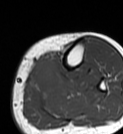
MRI of an extremity soft-tissue mass, one axial slice; slice 18 of 68 in the series (ordered by position); MR volume resampled by the dataset authors to the PET/CT grid (not the native acquisition matrix); 3.27 mm slice thickness; 123 × 134 image matrix, field of view 120 × 131 mm. Female patient. From the clinical record (not read from this slice): histological type: extraskeletal high grade osteogenic sarcoma; grade: high; site of the primary tumour: left calf.
Annotated regions visible in this slice (expert contour drawn on MRI and transferred to this co-registered scan by the dataset authors):
- gross tumour volume (mass): box from (x=29, y=61) to (x=55, y=90) px